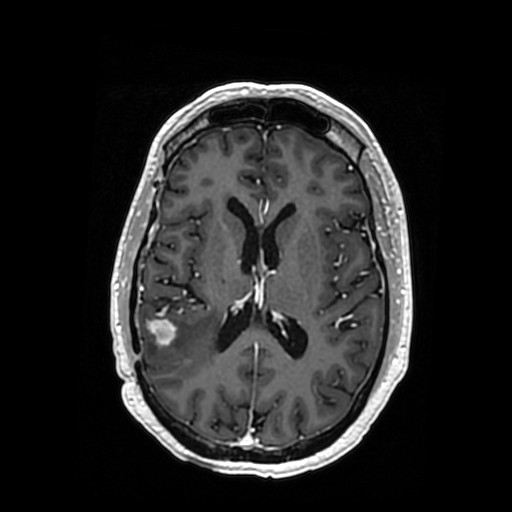
Brain MRI from a brain-tumour surgery series, one axial slice; position 165 of 364 along the scan axis; T1-weighted post-contrast; 0.5 mm slice thickness; 512 × 512 image matrix, field of view 260 × 260 mm. From the clinical record (not read from this slice): histopathology: Oligodendroglioma; WHO grade: 3; IDH mutation: yes; tumour location: Right Posterior Temporal Inferior Parietal.
Structures marked on this image (manually delineated by an expert):
- tumour: box from (x=173, y=318) to (x=201, y=346) px